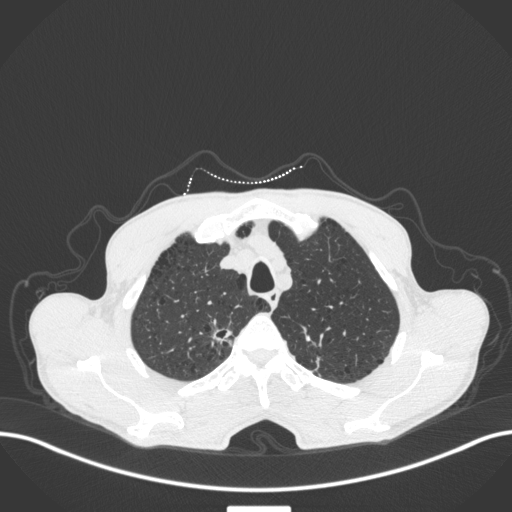
Chest CT, one axial slice; slice 360 of 445 in the series (ordered by position); 120 kVp; lung window (W 1500 / L -600 HU); 512 × 512 image matrix. Male patient, age 70 years. Case-level facts recorded for this patient, not image findings: clinical TNM (as recorded): T1a N0 M0.
Outlined on this slice (rectangle marked by the reading radiologist):
- lung tumour (recorded histology: adenocarcinoma): bounding box <204,316,234,352> (left, top, right, bottom; pixels)